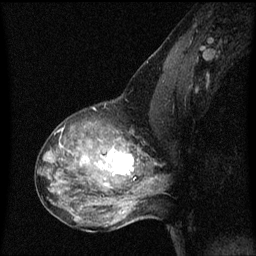
Breast MRI (dynamic contrast-enhanced), one sagittal slice; slice 37 of 60 in the series (ordered by position); dynamic contrast-enhanced series, image 2 of 3 at this slice position (ordered by acquisition); 1.5 T; TE 4.2 ms, TR 8 ms; 2 mm slice thickness; 256 × 256 image matrix, field of view 200 × 200 mm. Female patient, age 50 years.
Annotated regions visible in this slice (semi-automatic segmentation, software-assisted and operator-edited):
- analysis volume of interest (the breast-tissue region the enhancement analysis was run in; not a lesion): bounding box <91,126,141,189> (left, top, right, bottom; pixels)
- tumour enhancement mask (voxels above the 70 % enhancement threshold inside the analysis volume of interest): <100,146,134,177>